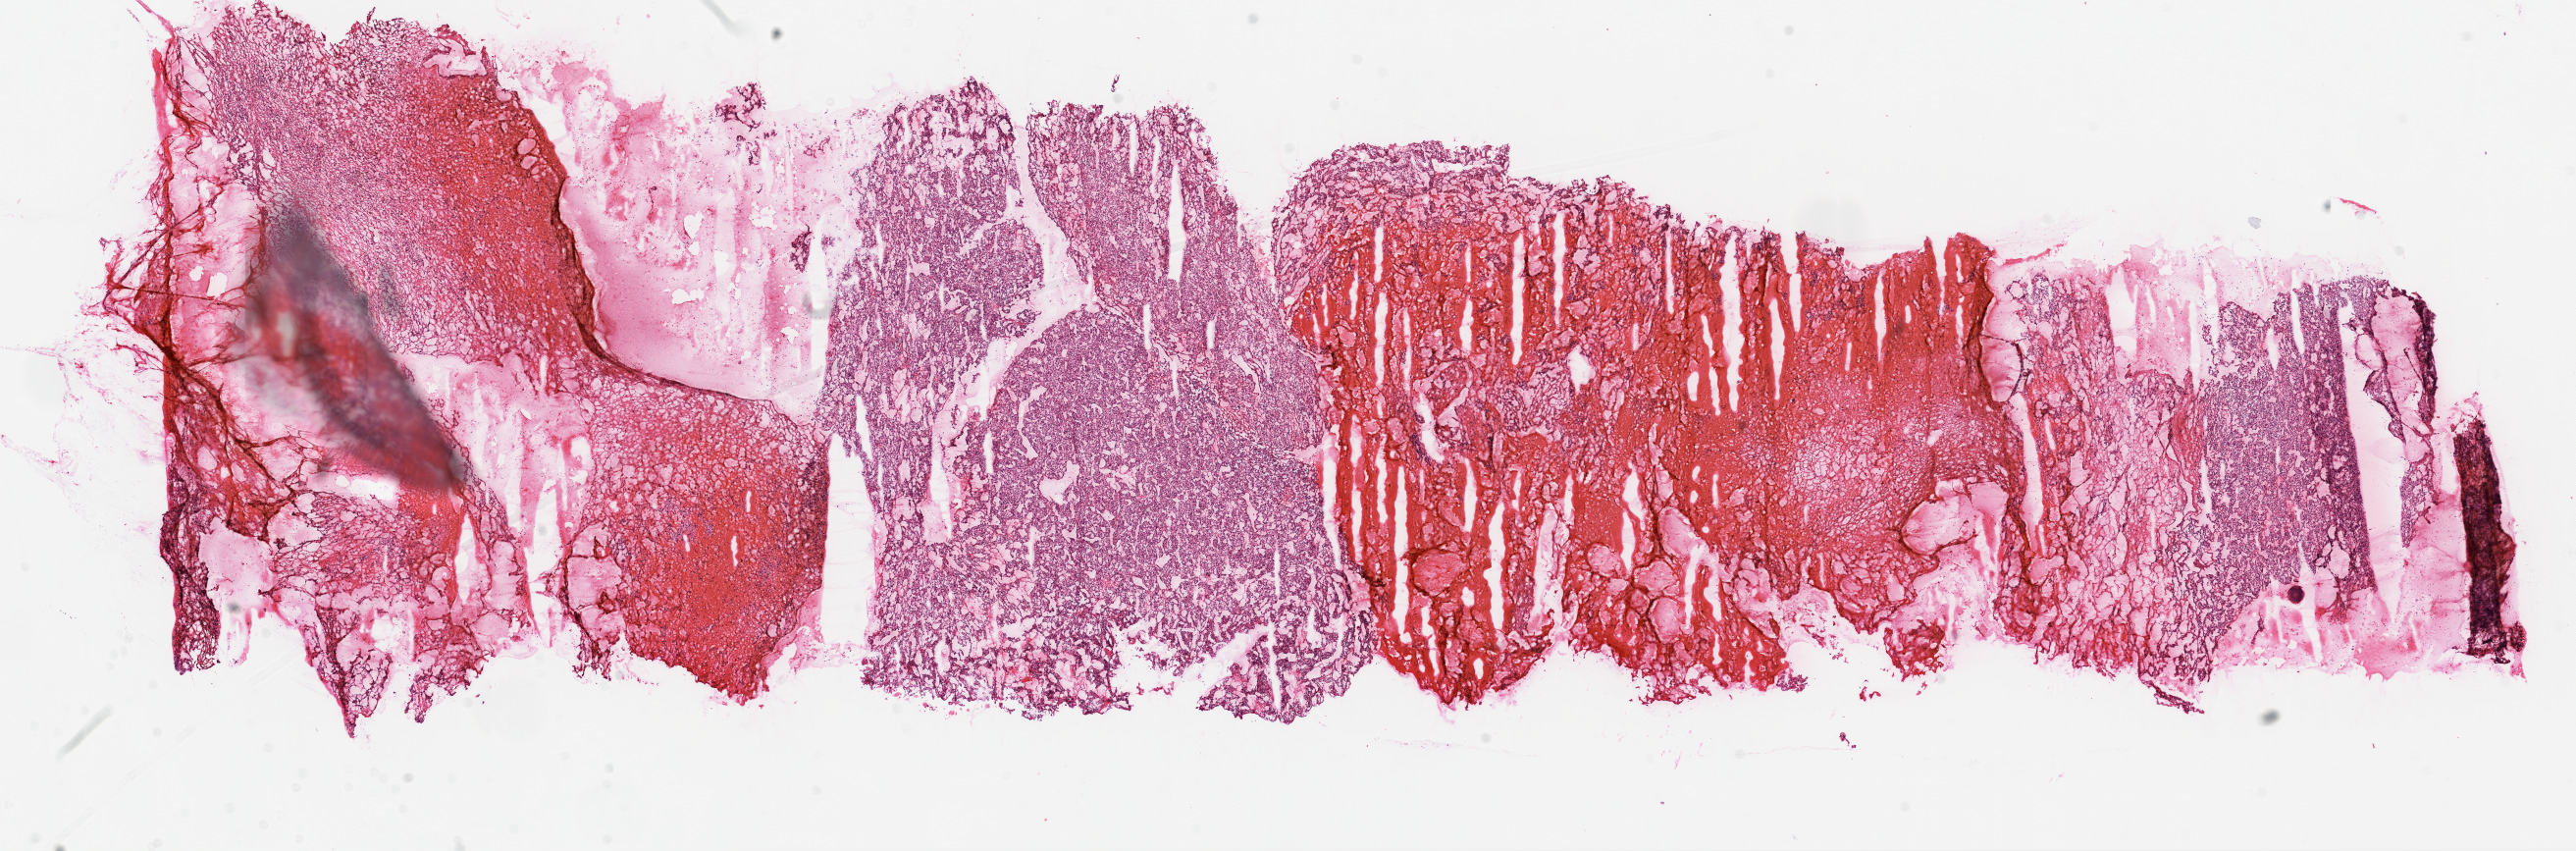
Digitized H&E-stained tissue section (whole slide), a low-resolution overview of the entire scanned area, about 21.1 x 7.0 mm, frozen section from the top of the tissue portion, kidney, primary tumour sample. Female, age 60 years at initial diagnosis. Histologic grade: G2 (moderately differentiated). Composition of this section per pathologist review: tumour cells 70%, tumour nuclei 80%, normal cells 0%, stromal cells 30%, necrosis 0%.
Laterality: right. AJCC pathologic stage: I (7th edition). Histologic diagnosis: Clear cell adenocarcinoma, NOS. TNM: T1b NX M0.